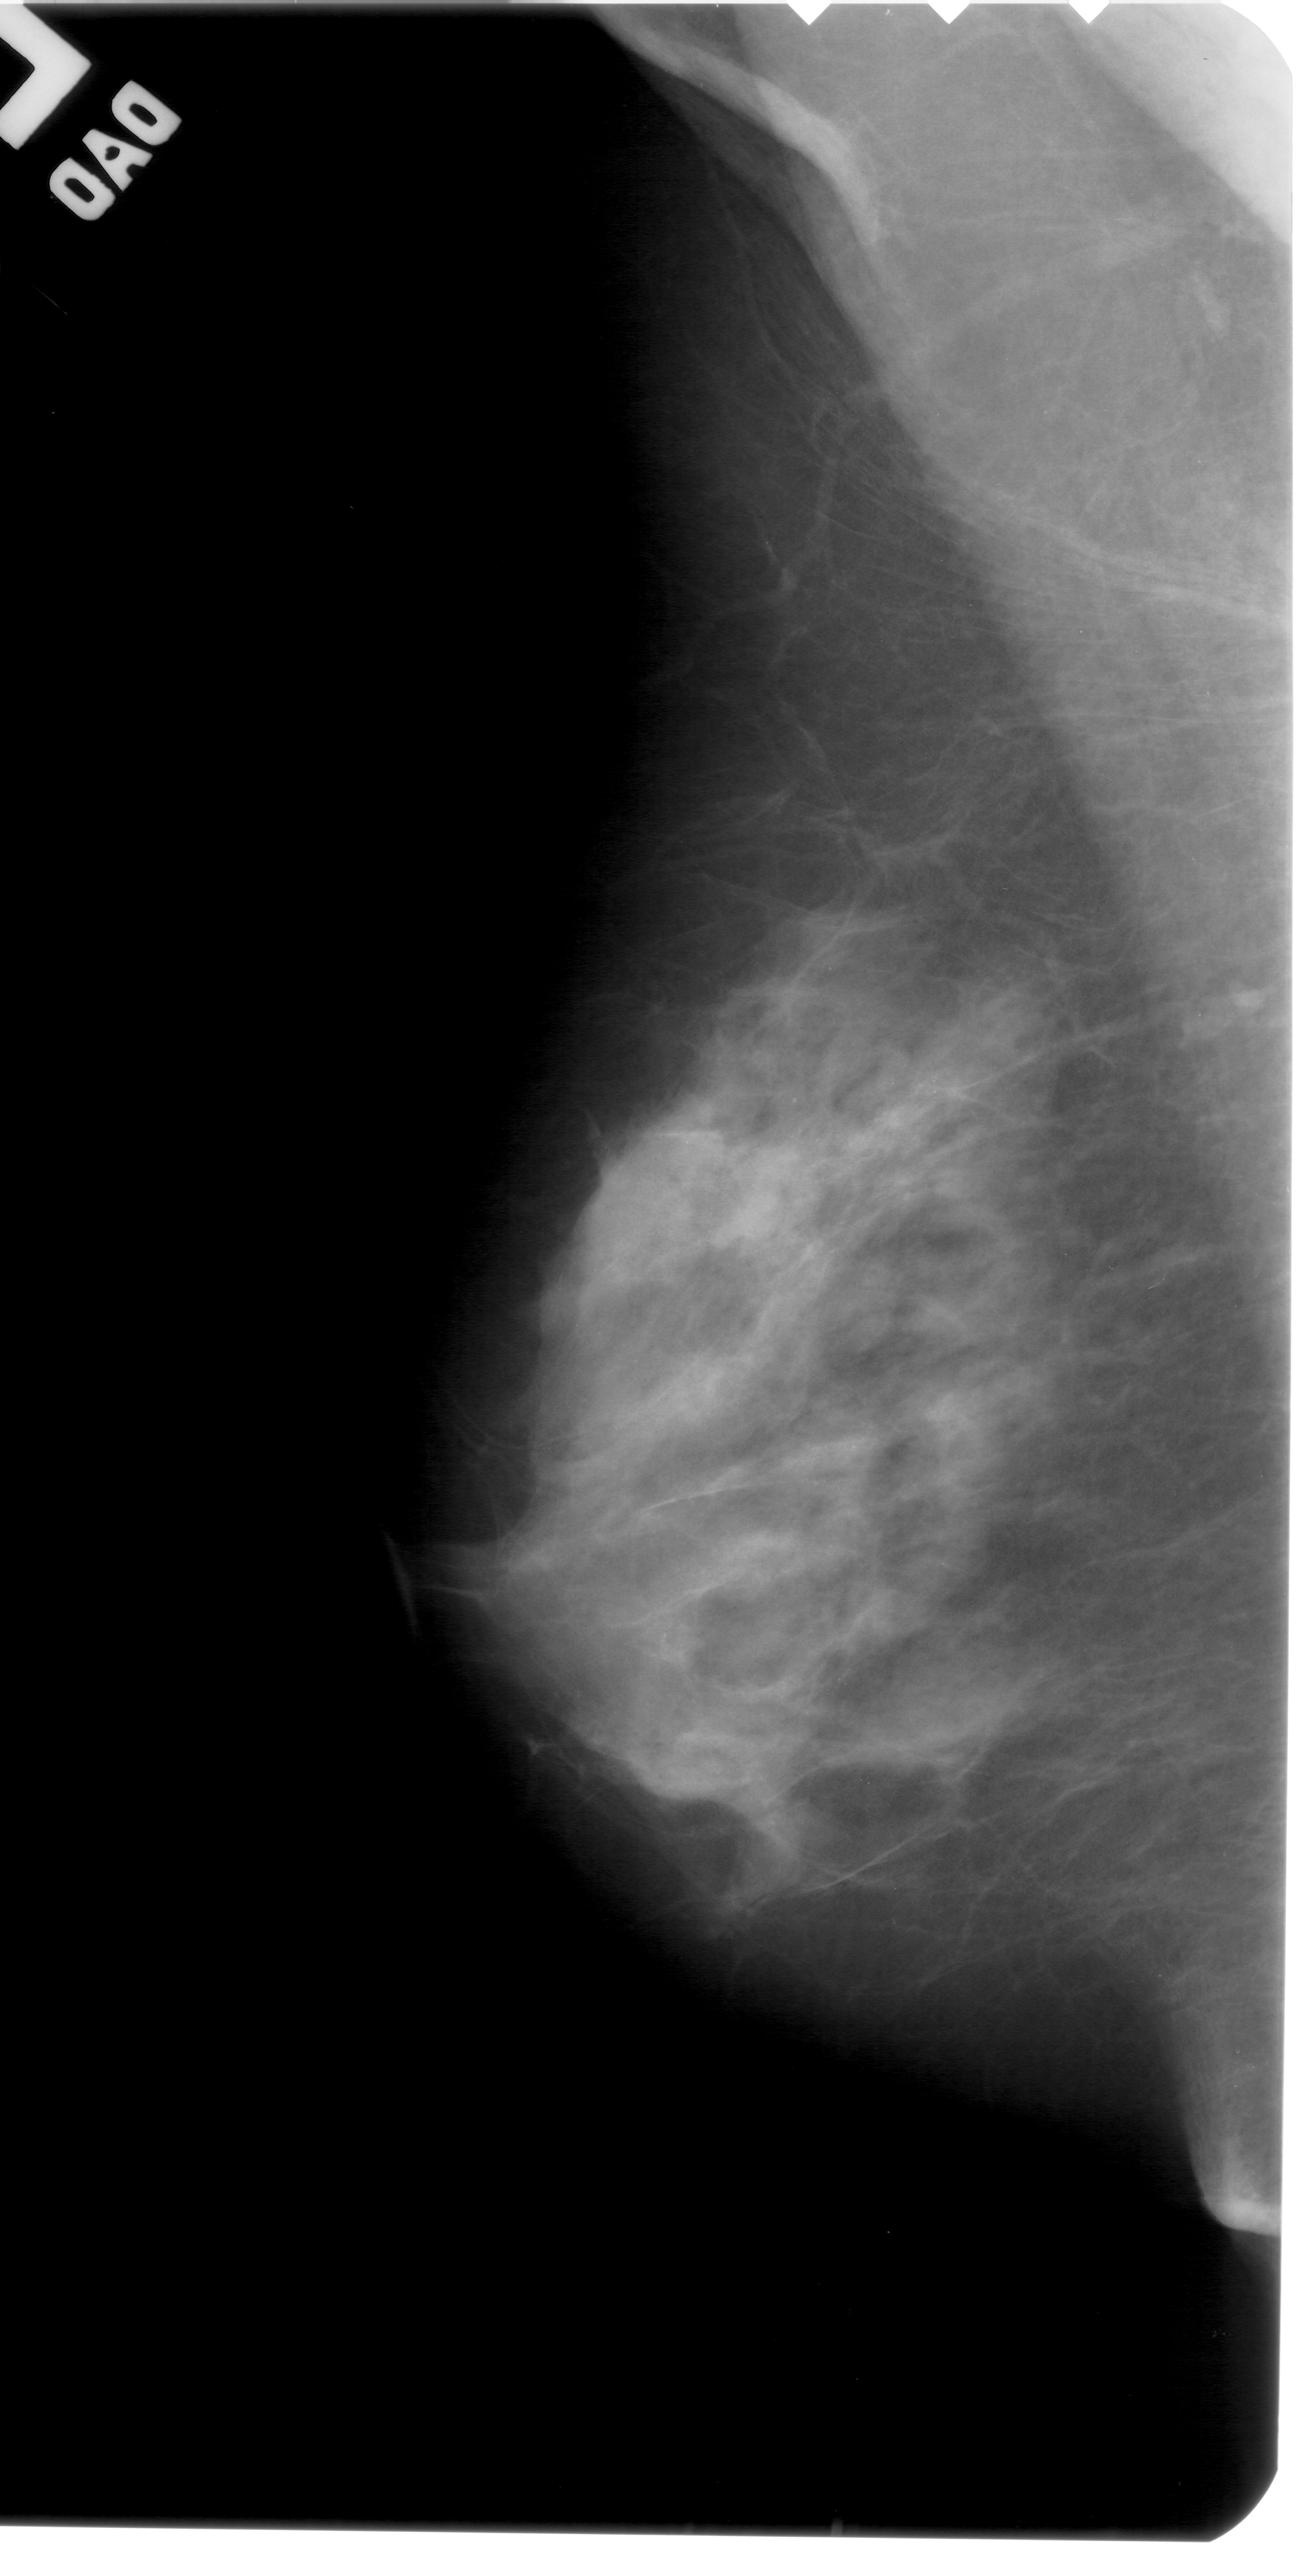
Digitized screen-film mammogram; left breast; MLO view; breast composition: extremely dense (BI-RADS density category 4 of 4).
- Finding: calcifications, morphology punctate, distribution linear; BI-RADS assessment category 4; subtlety rating 1 on a 1 (subtle) to 5 (obvious) scale; pathology result (as recorded, not read from the image): benign.